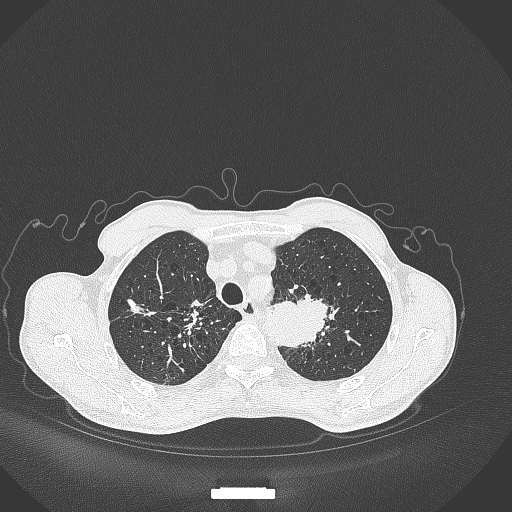
Chest CT, one axial slice. Position 346 of 386 along the scan axis. Reconstruction kernel B70f. Lung window (W 1500 / L -600 HU). 1 mm slice thickness. 512 × 512 image matrix. Patient: male, 65 years. Case-level facts recorded for this patient, not image findings: clinical TNM (as recorded): T2b N0 M0.
Outlined on this slice (rectangle marked by the reading radiologist):
- lung tumour (recorded histology: adenocarcinoma): bounding box <265,291,333,350> (left, top, right, bottom; pixels)